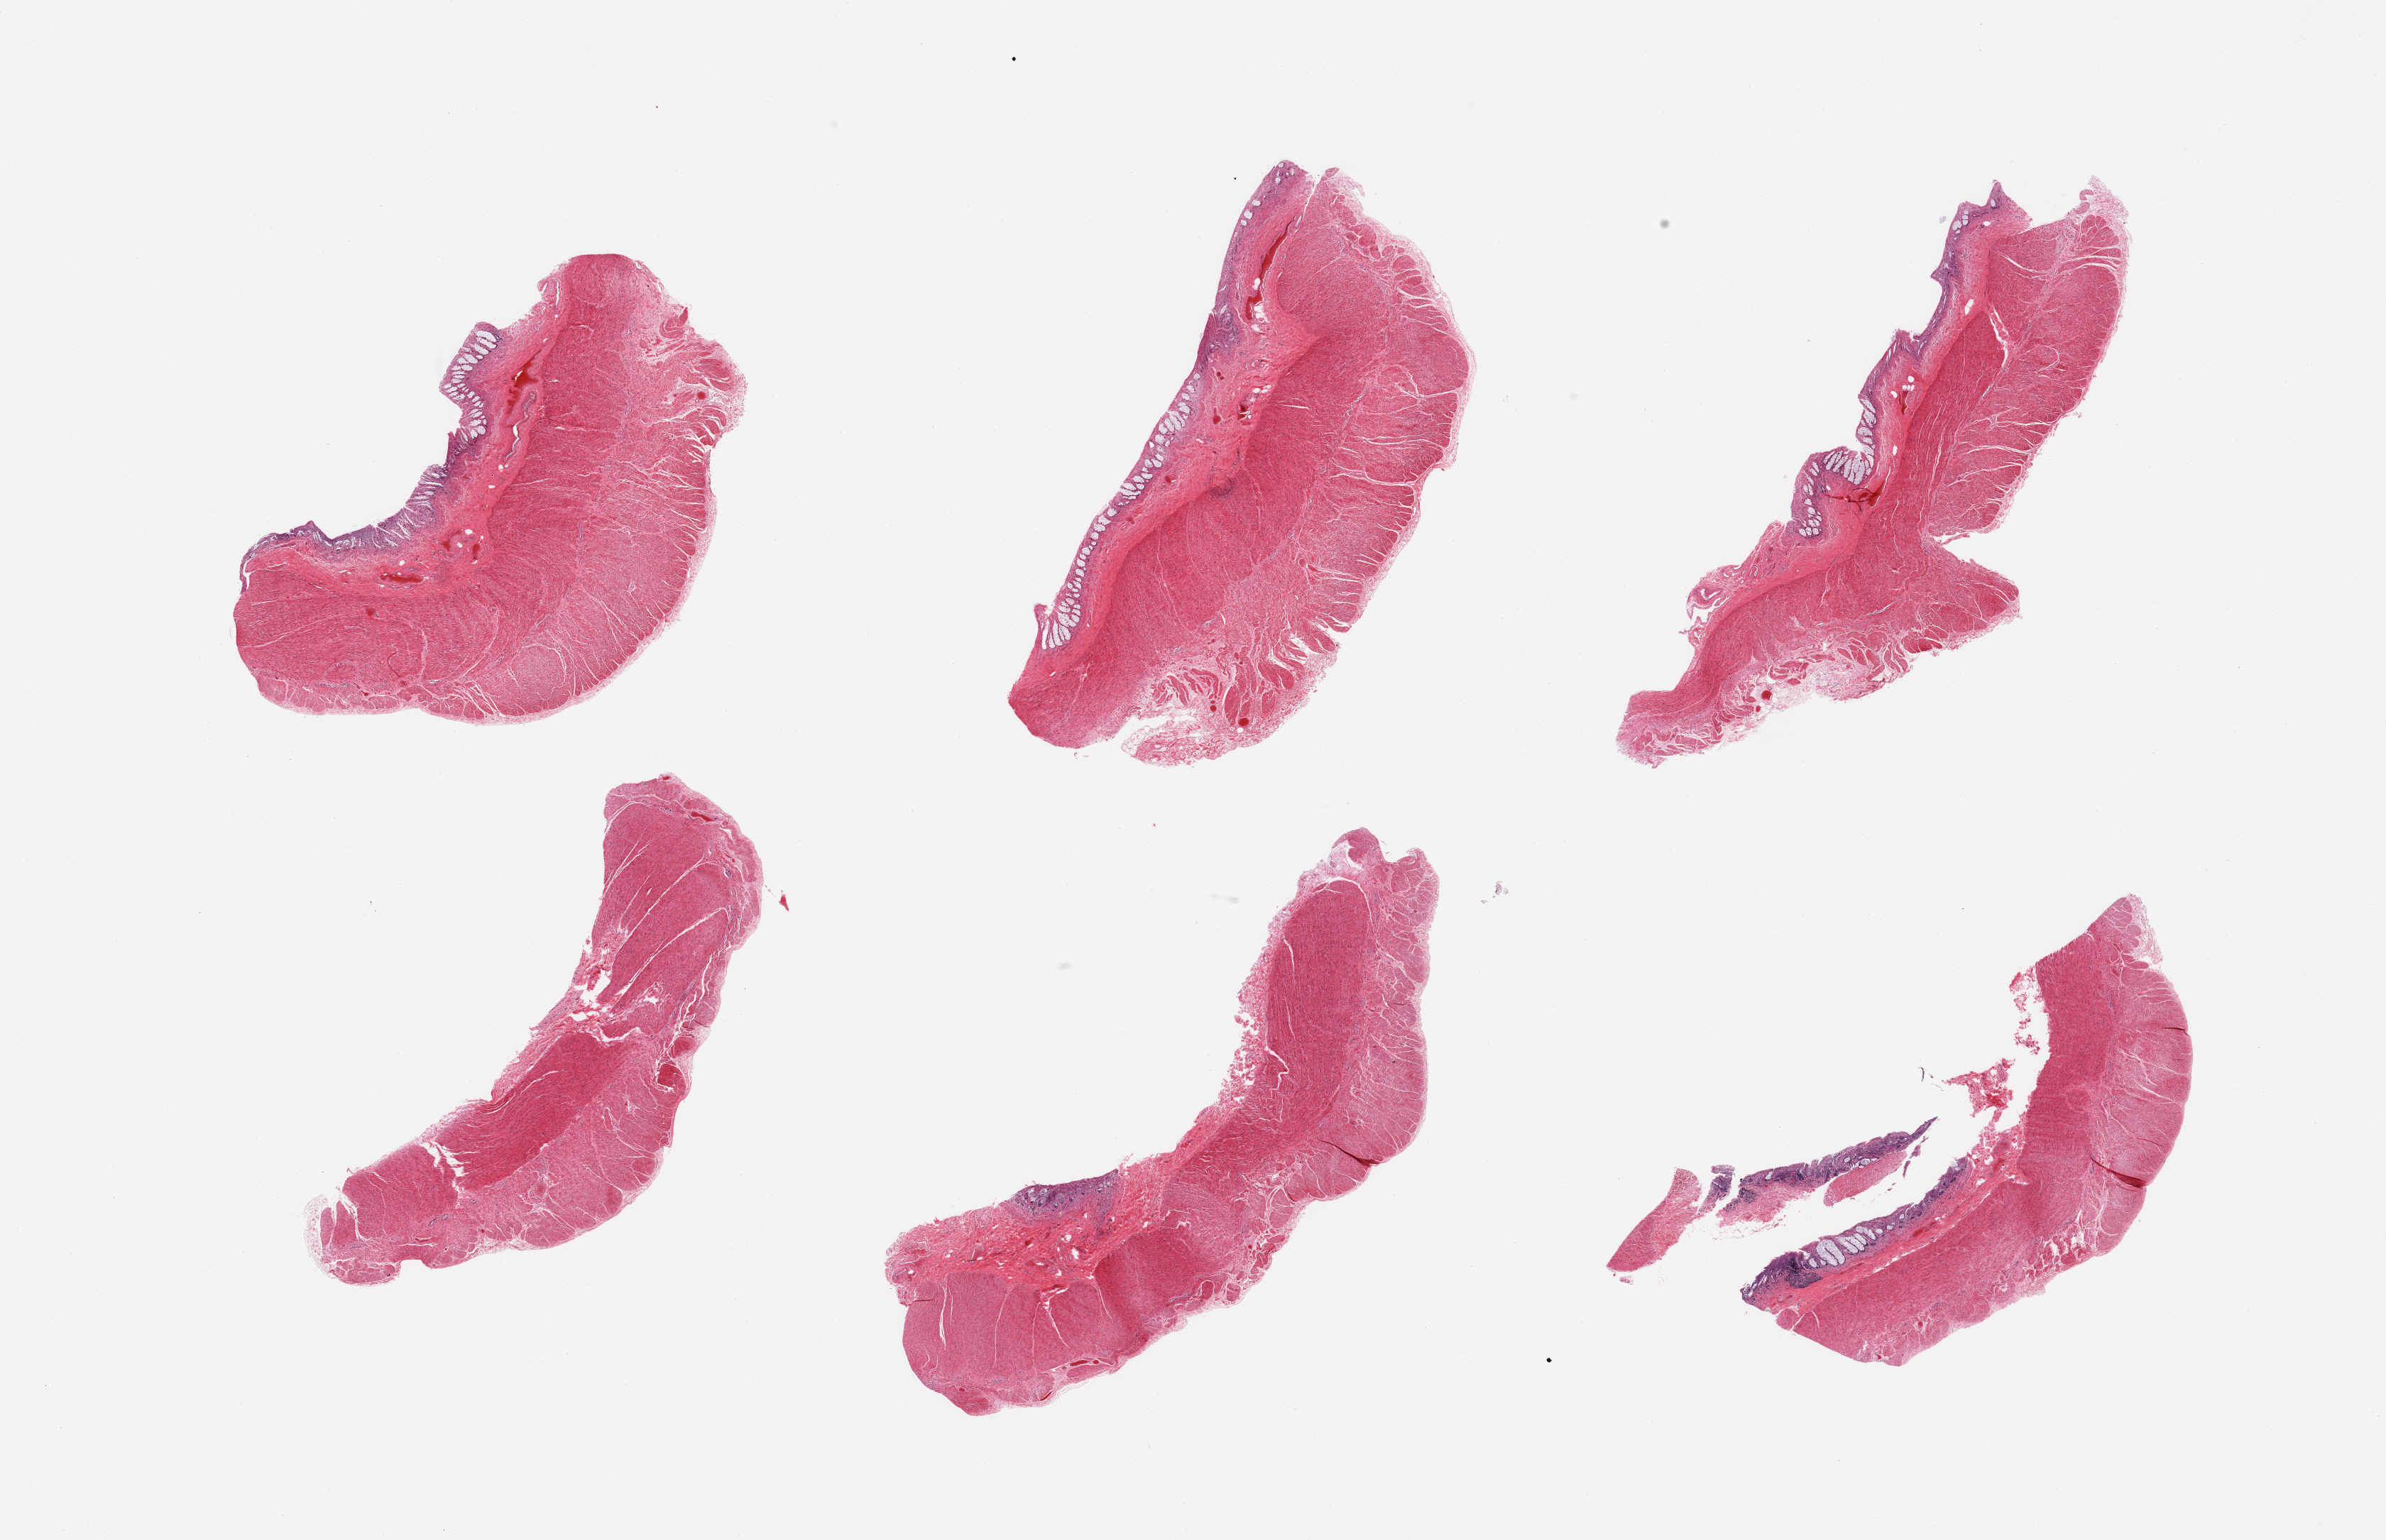
Digitized hematoxylin and eosin (H&E)-stained section, brightfield, low-resolution overview of the scanned area, about 26.6 x 17.2 mm (acquisition: 20x scan). PAXgene-fixed paraffin-embedded (PFPE) section. Sampled site (target tissue): sigmoid colon. Tissue donor sample. Female donor.
- review note (as recorded): 6 pieces; 5 of 6 have mucosa as well as muscularis